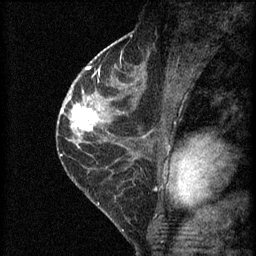
Breast MRI (dynamic contrast-enhanced), one sagittal slice. Position 34 of 60 along the scan axis. 3 images stored at this slice position (order not interpretable as contrast timing). 1.5 T. TE 4.2 ms, TR 8.2 ms. 2 mm slice thickness. 256 × 256 image matrix. Female patient, age 45 years.
Annotated regions visible in this slice (semi-automatic segmentation, software-assisted and operator-edited):
- analysis volume of interest (the breast-tissue region the enhancement analysis was run in; not a lesion): box from (x=62, y=98) to (x=104, y=139) px
- tumour enhancement mask (voxels above the 70 % enhancement threshold inside the analysis volume of interest): (x=62, y=98)–(x=98, y=131)